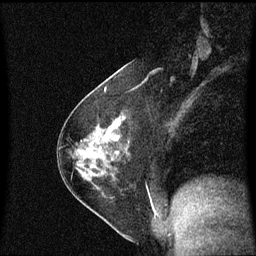
Breast MRI (dynamic contrast-enhanced), one sagittal slice. Slice 33 of 60 in the series (ordered by position). Dynamic contrast-enhanced series, image 2 of 3 at this slice position (ordered by acquisition). 1.5 T. TE 4.2 ms, TR 8.4 ms. 256 × 256 image matrix. Female patient, age 54 years. Case-level facts recorded for this patient, not image findings: setting: breast cancer imaged before/during neoadjuvant chemotherapy; receptor status: HER2-positive.
Structures marked on this image (semi-automatically segmented with operator editing):
- analysis volume of interest (the breast-tissue region the enhancement analysis was run in; not a lesion): bounding box [x1, y1, x2, y2] px = [62, 119, 130, 189]
- tumour enhancement mask (voxels above the 70 % enhancement threshold inside the analysis volume of interest): [115, 121, 121, 141]